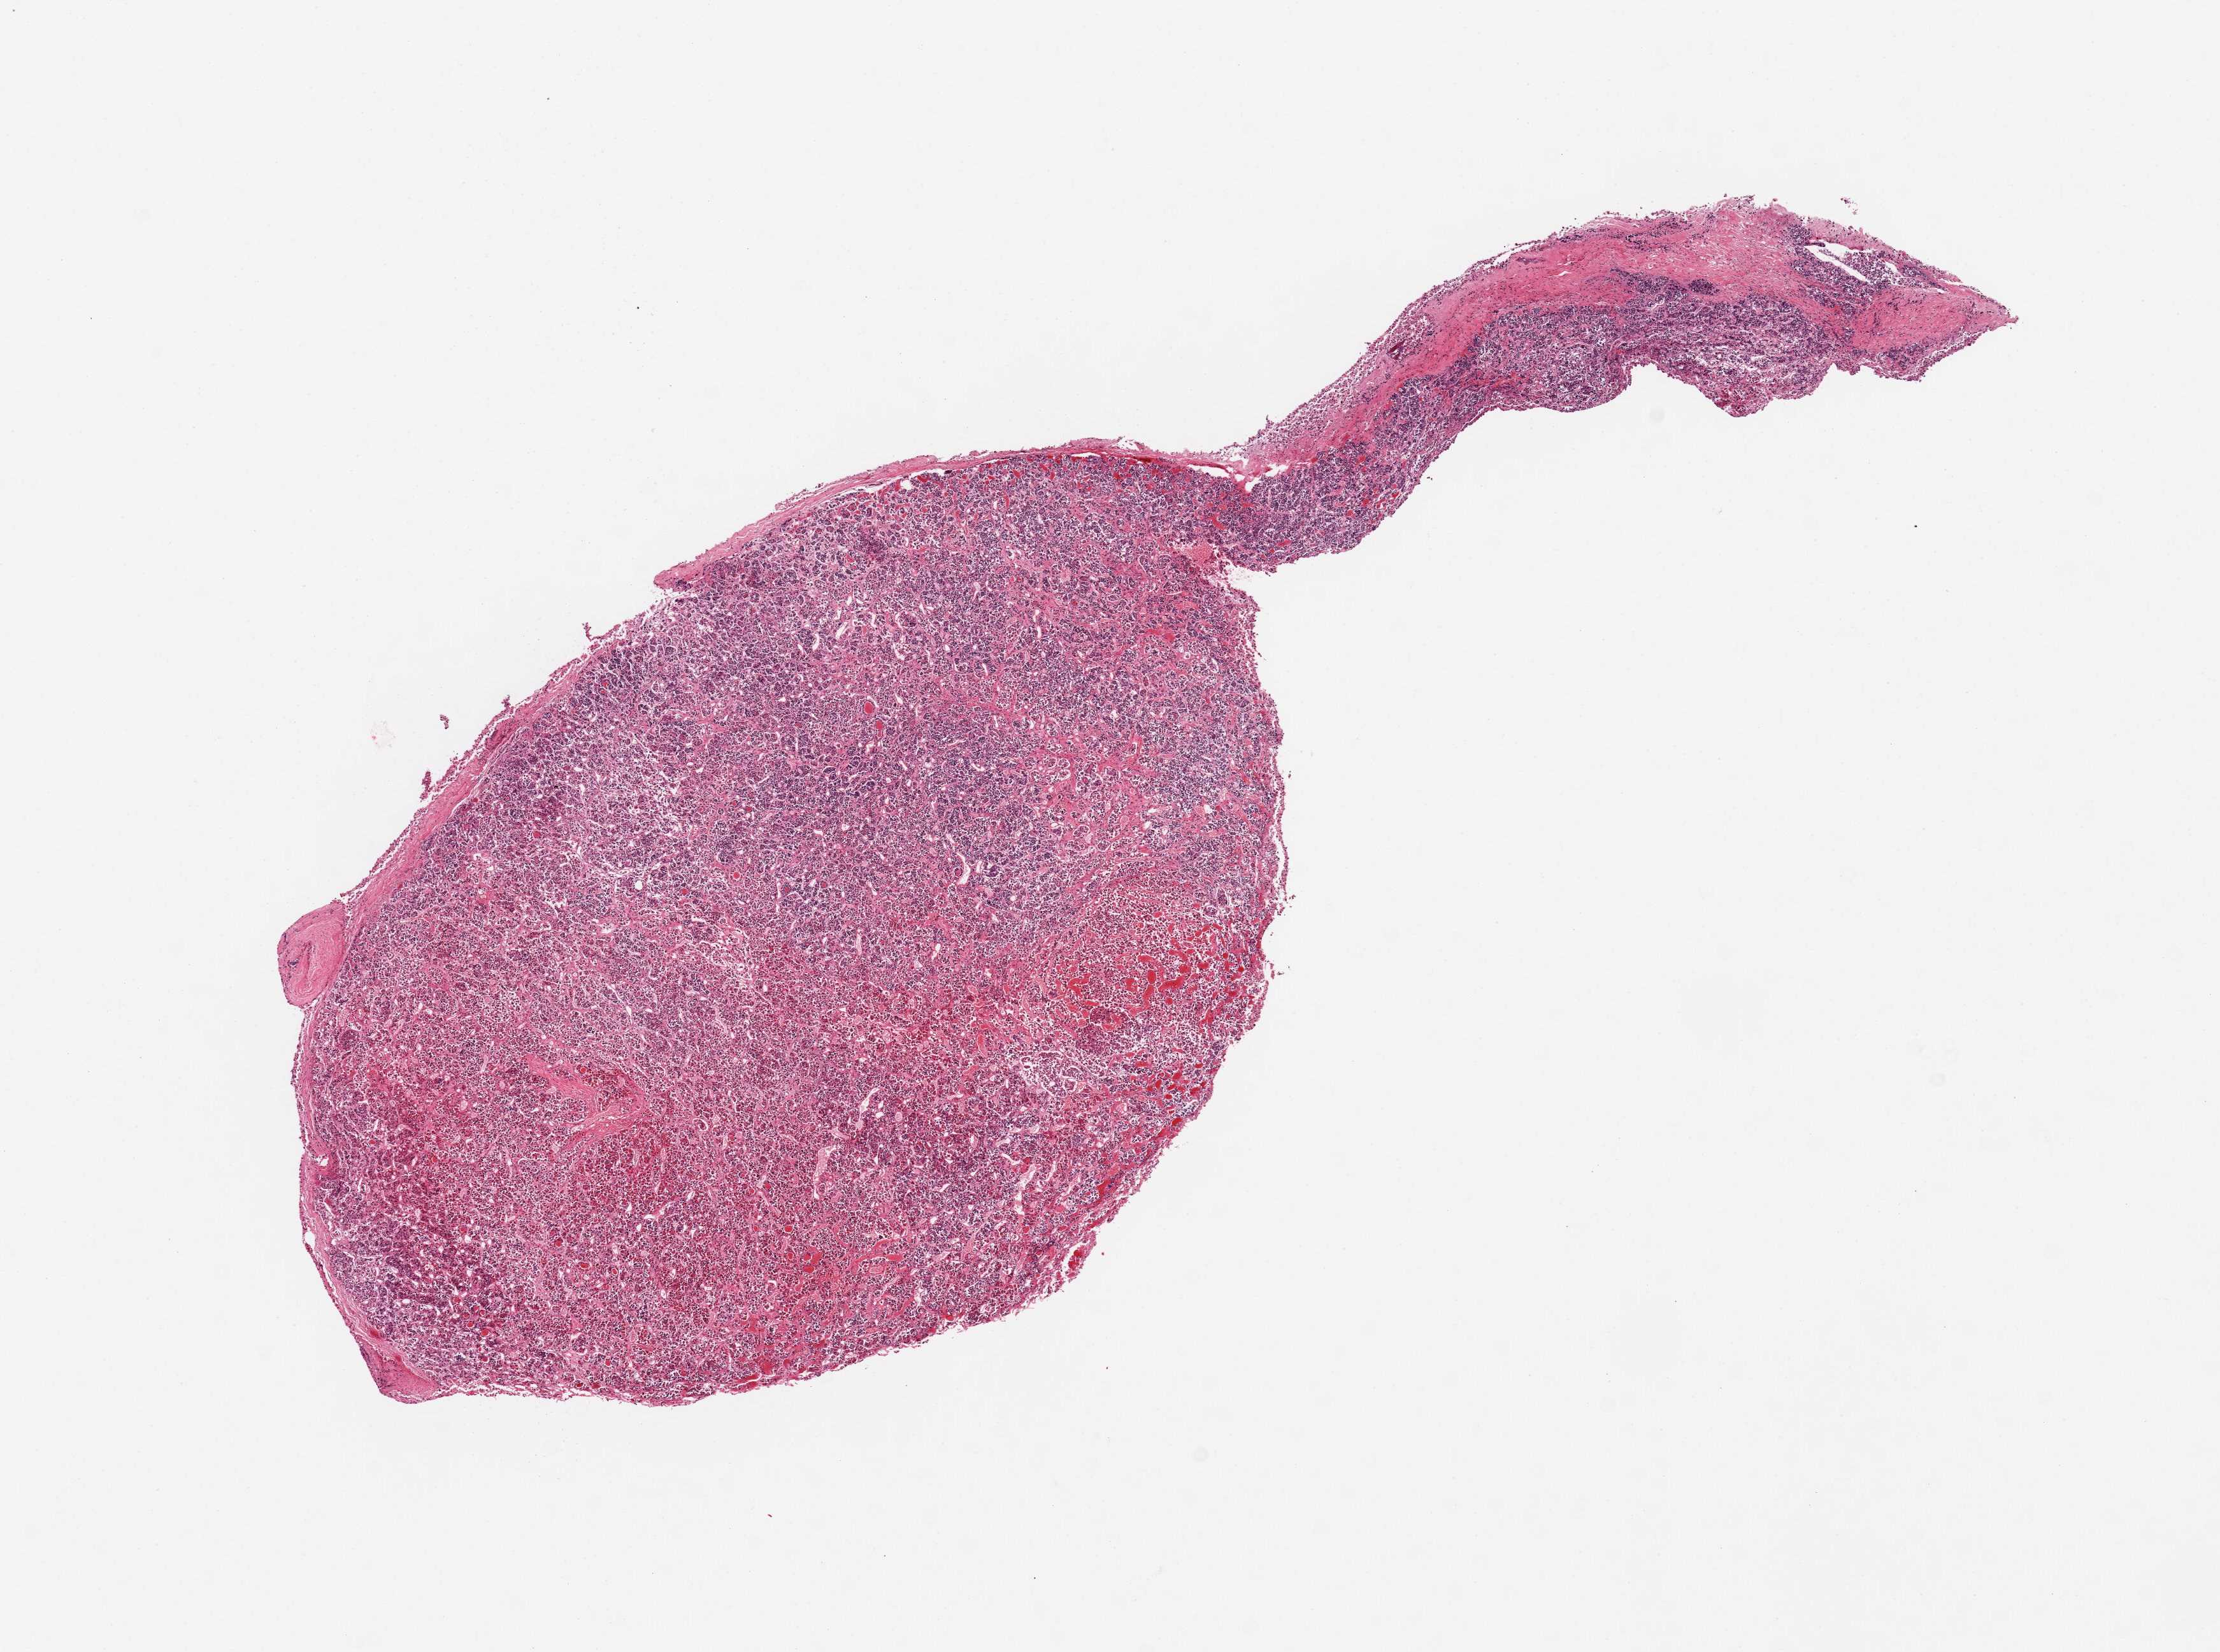
Digitized hematoxylin and eosin (H&E)-stained section — a low-resolution overview of the entire scanned area, about 13.8 x 10.3 mm (acquisition: 20x scan); PAXgene-fixed paraffin-embedded (PFPE) section; section of pituitary (target tissue); donor tissue sample. Donor sex: male.
Review note (as recorded): 1 piece; adenohypophysis.